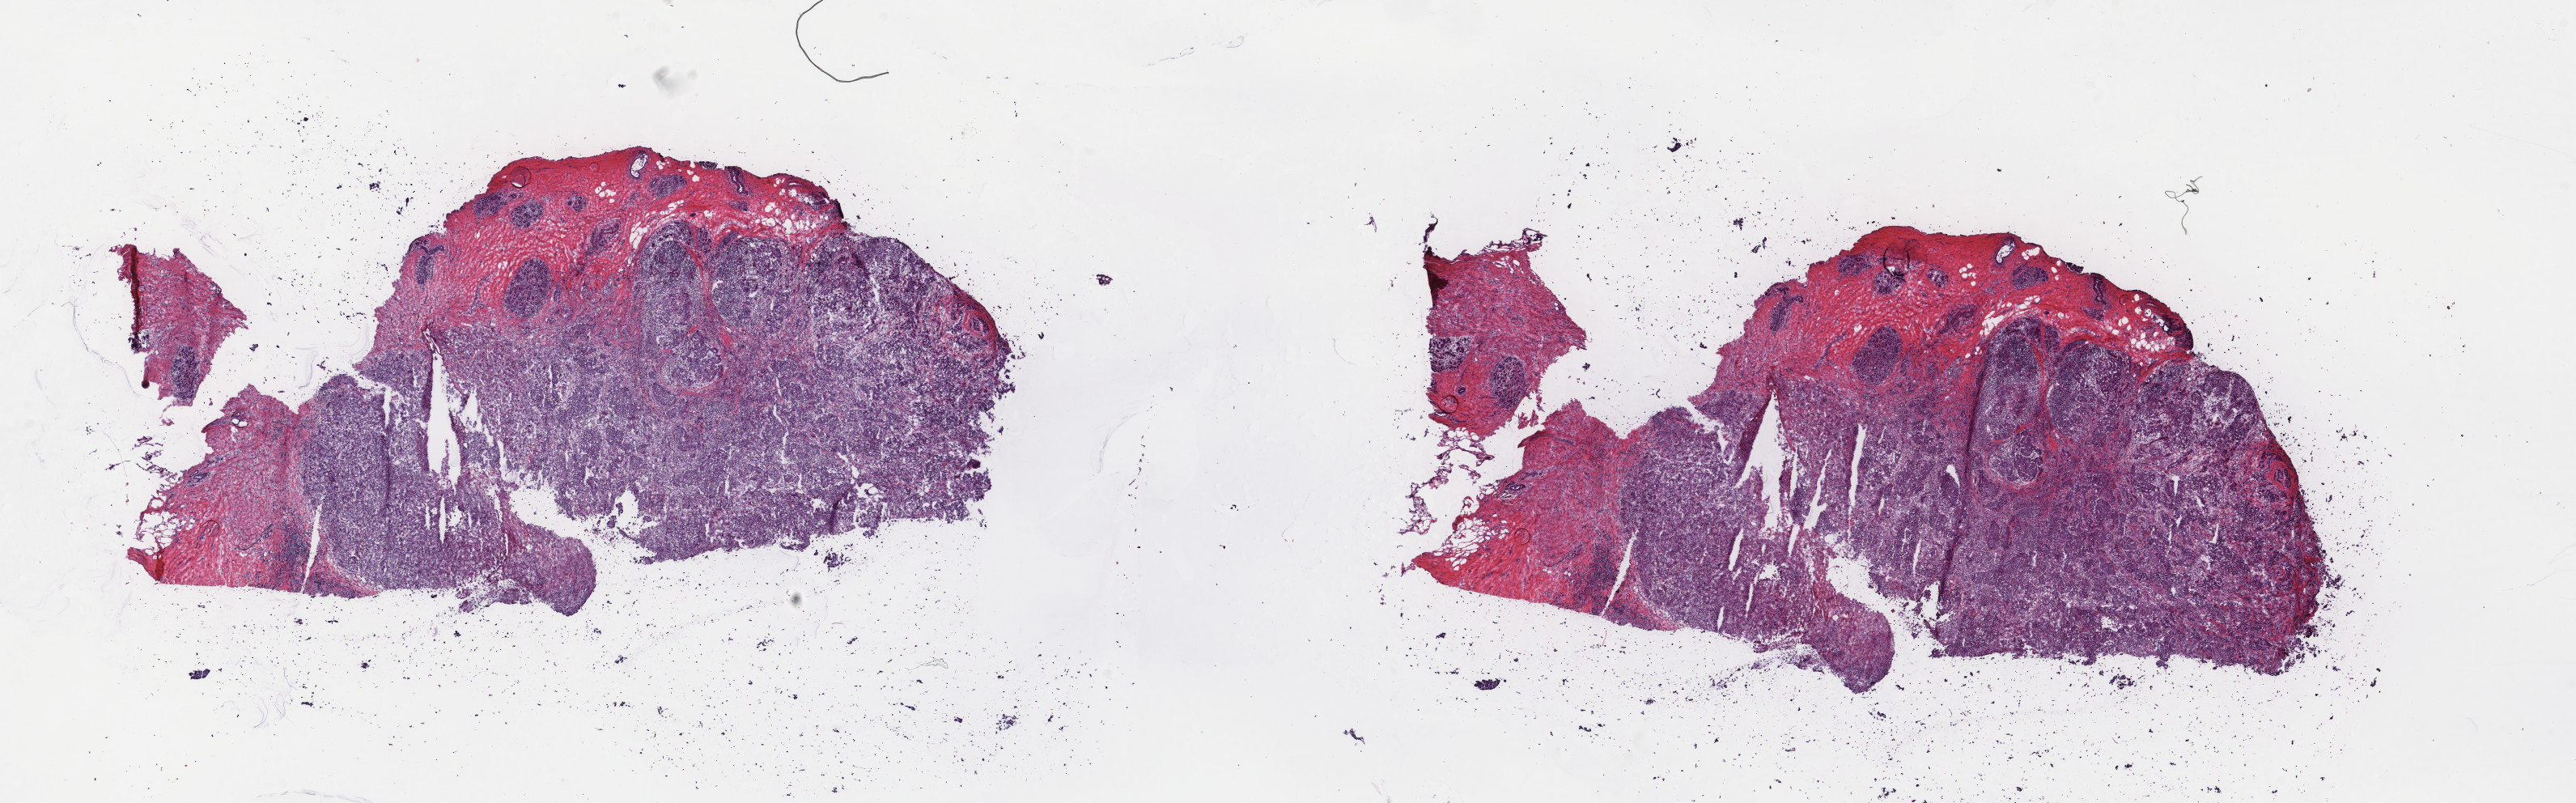
Digitized H&E tissue section (whole slide) — low-resolution overview of the scanned area, about 25.3 x 7.9 mm, frozen section from the top of the tissue portion, primary tumour sample from the breast. Patient: female, age at initial diagnosis 47 years. Composition of this section per pathologist review: tumour cells 80%, tumour nuclei 80%, normal cells 8%, stromal cells 10%, necrosis 2%. Infiltration values recorded for this section: lymphocyte infiltration 0%, monocyte infiltration 0%, neutrophil infiltration 0%.
* lymph nodes positive (case pathology): 2 of 39 examined
* AJCC pathologic stage: IIA
* histologic diagnosis: Infiltrating duct carcinoma, NOS